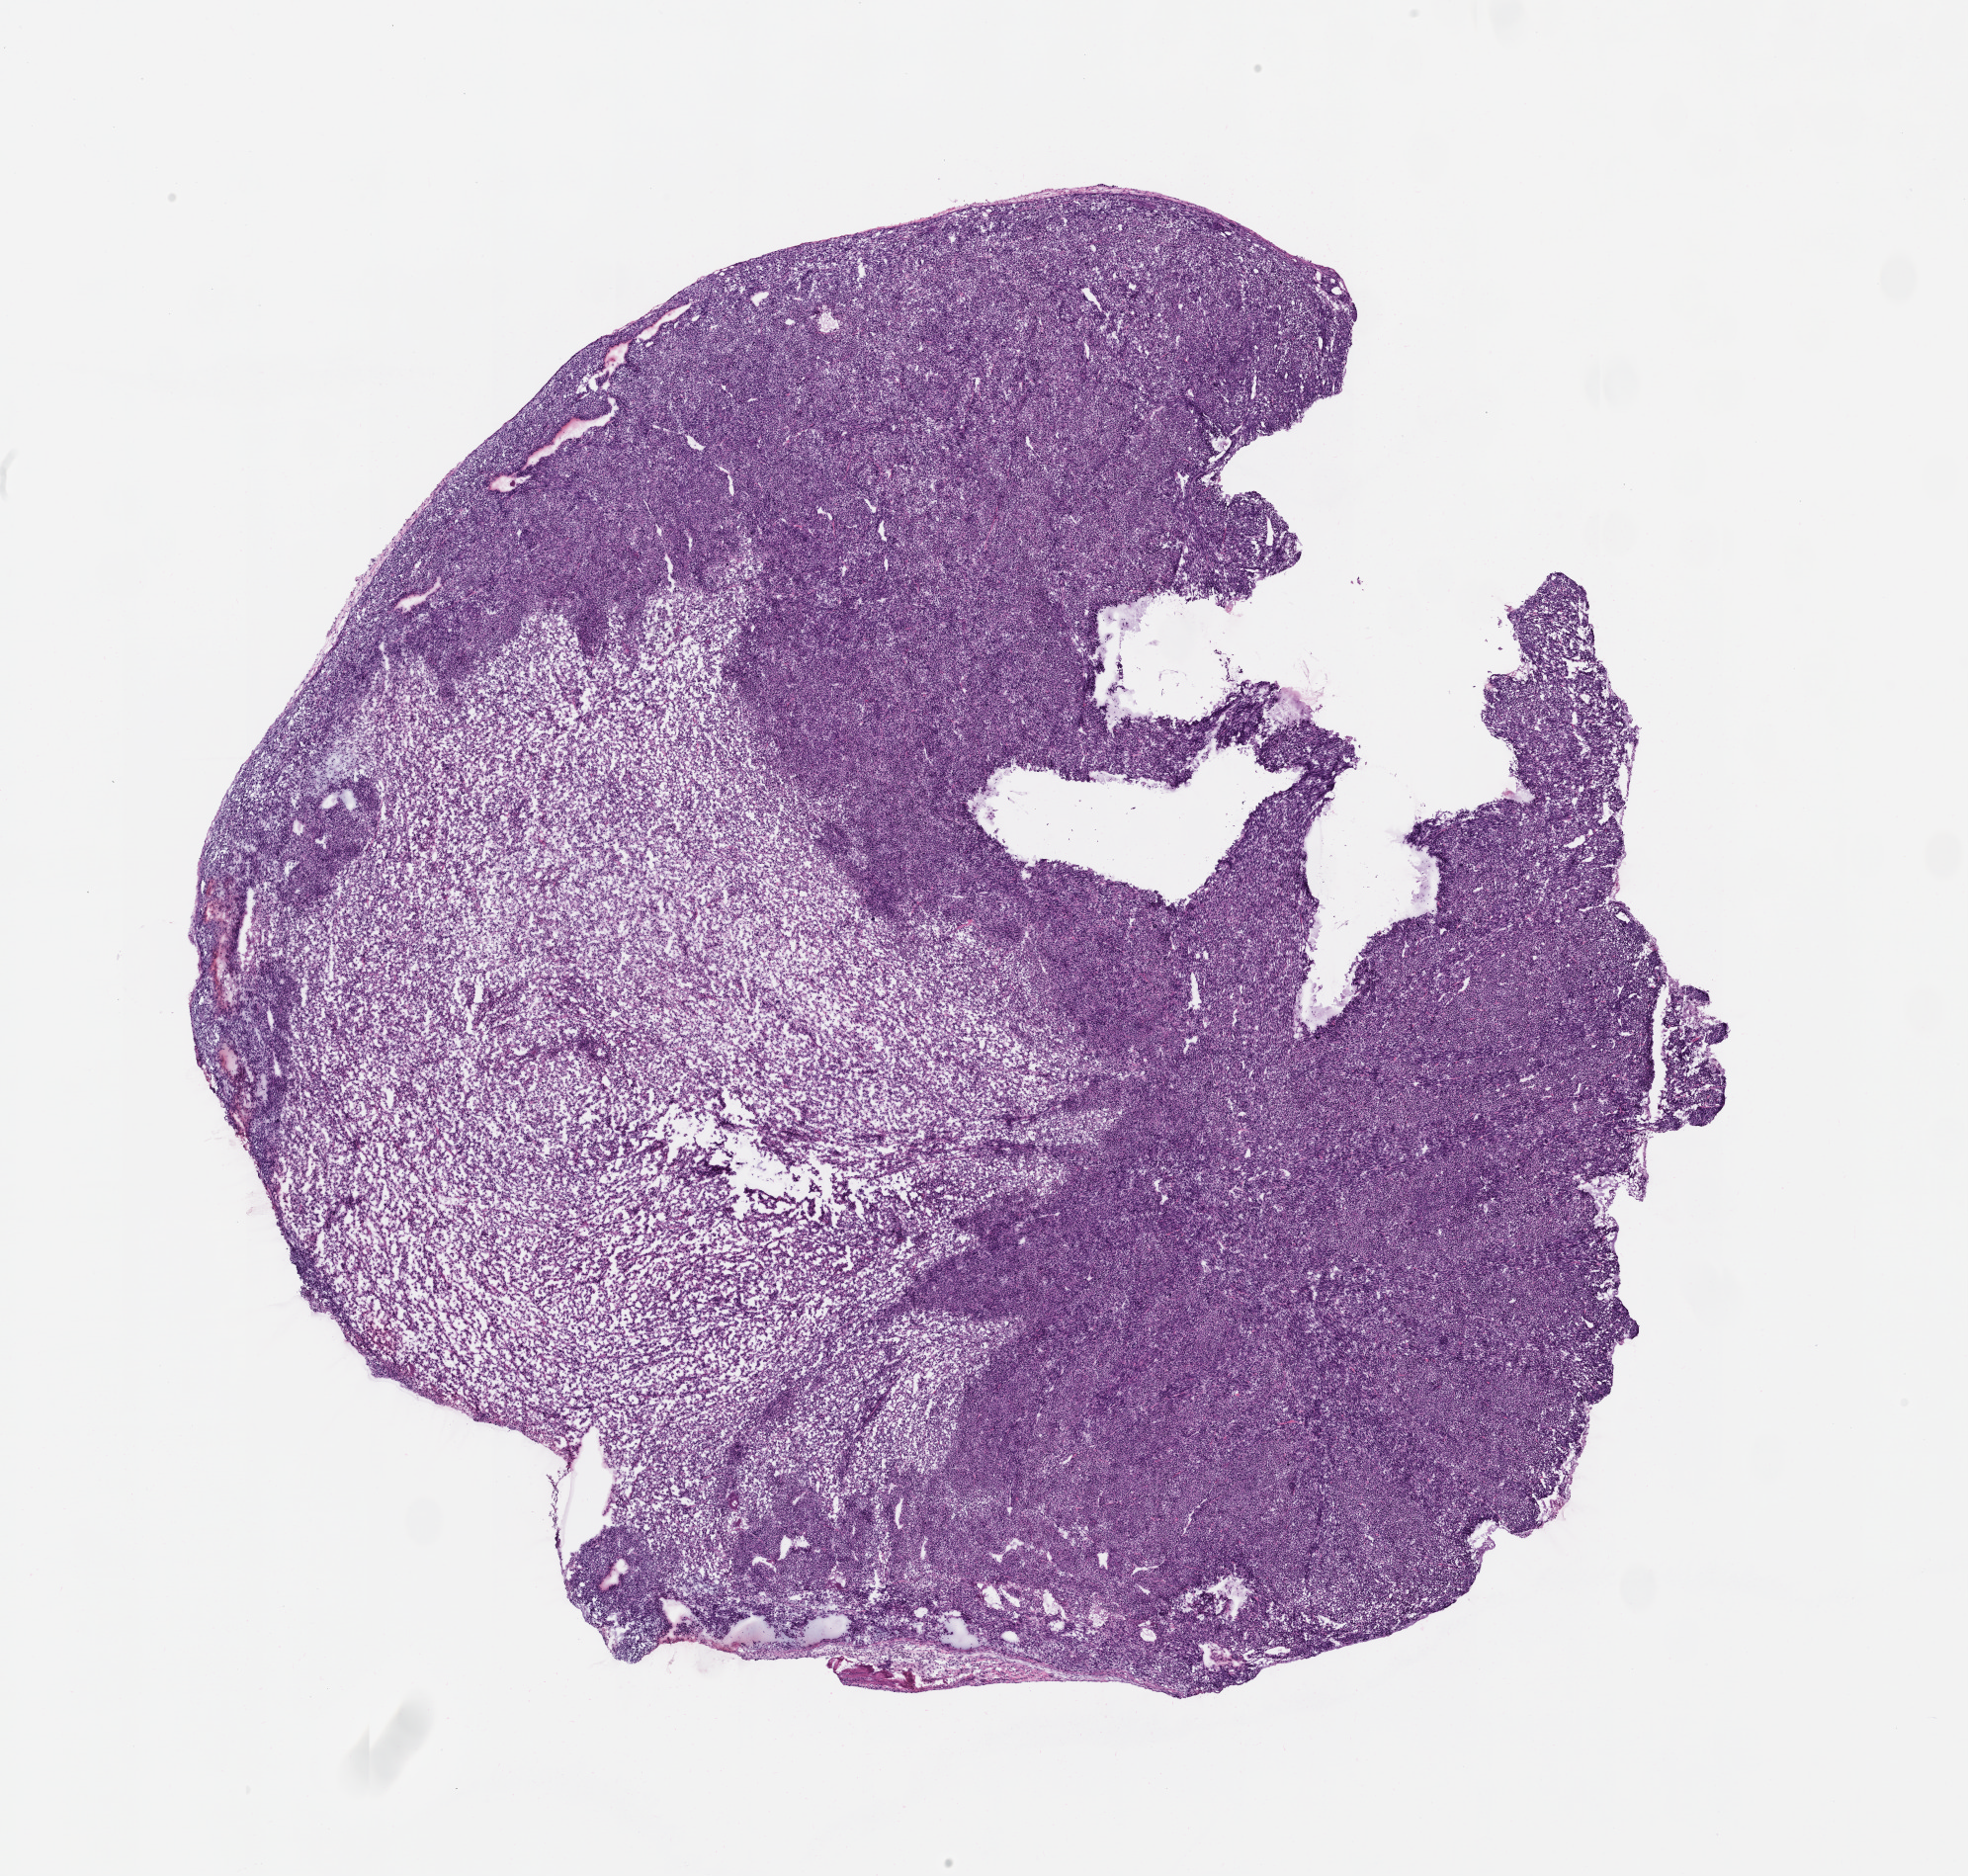
Haematoxylin and eosin whole-slide image of a patient-derived xenograft (PDX) tumor grown in a mouse, passage 1, low-resolution overview of the scanned area, about 16.0 x 15.2 mm, formalin-fixed, paraffin-embedded (FFPE) tissue, originating tumor site category: uterus.
Originating patient diagnosis: Leiomyosarcoma.